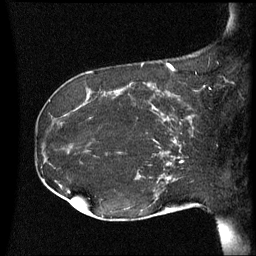
Breast MRI (dynamic contrast-enhanced), one sagittal slice. Position 25 of 60 along the scan axis. Dynamic contrast-enhanced series, image 2 of 3 at this slice position (ordered by acquisition). 1.5 T. TE 4.2 ms, TR 8.4 ms. 256 × 256 image matrix, field of view 220 × 220 mm. Patient: female, 41 years. From the clinical record (not read from this slice): setting: breast cancer imaged before/during neoadjuvant chemotherapy; receptor status: HER2-positive.
Structures marked on this image (semi-automatically segmented with operator editing):
- analysis volume of interest (the breast-tissue region the enhancement analysis was run in; not a lesion): bounding box <122,84,195,137> (left, top, right, bottom; pixels)
- tumour enhancement mask (voxels above the 70 % enhancement threshold inside the analysis volume of interest): <151,86,193,137>